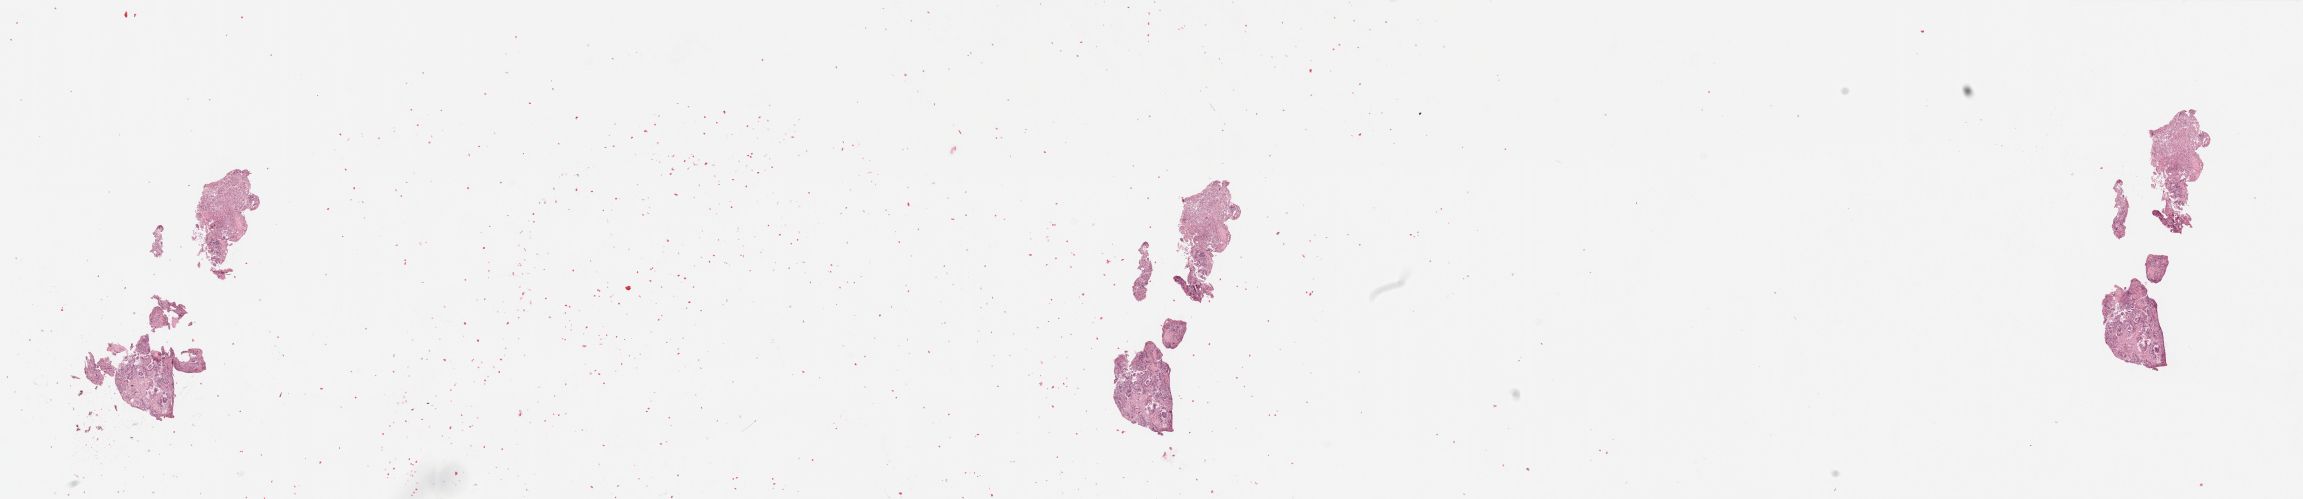
H&E-stained whole-slide image, shown as a low-resolution overview of the whole scanned area (about 36.4 x 7.9 mm); lung, tumour tissue. Patient: male, age 66 years. Histologic grade: G2 (moderately differentiated).
AJCC pathologic stage: IB. Primary tumour site (as recorded): left lower lobe. Diagnosis: Adenocarcinoma, NOS.